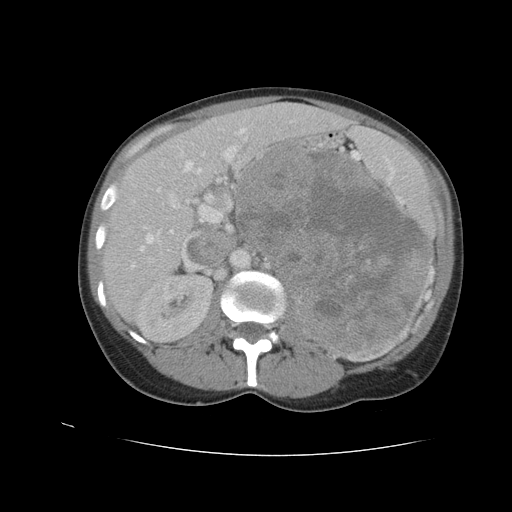
Contrast-enhanced abdominal CT, one axial slice. Reconstruction kernel STANDARD. 120 kVp. Intravenous contrast given. Soft-tissue window (W 400 / L 40 HU). 5 mm slice thickness. 512 × 512 image matrix. Female patient. From the clinical record (not read from this slice): diagnosis: adrenocortical carcinoma; tumour side: left adrenal; tumour size at pathology: 18 cm; Ki-67 index: 11 %; stage (as recorded): 3.
Outlined on this slice (semi-automatically segmented with operator editing):
- mass: box from (x=241, y=147) to (x=428, y=349) px